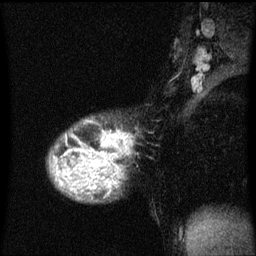
Breast MRI (dynamic contrast-enhanced), one sagittal slice. Slice 39 of 60 in the series (ordered by position). Dynamic contrast-enhanced series, image 2 of 3 at this slice position (ordered by acquisition). 1.5 T. TE 4.2 ms, TR 8 ms. 2 mm slice thickness. 256 × 256 image matrix. Female patient, age 36 years.
Annotated regions visible in this slice (semi-automatically segmented with operator editing):
- analysis volume of interest (the breast-tissue region the enhancement analysis was run in; not a lesion): box from (x=50, y=132) to (x=124, y=169) px
- tumour enhancement mask (voxels above the 70 % enhancement threshold inside the analysis volume of interest): (x=65, y=132)–(x=122, y=169)